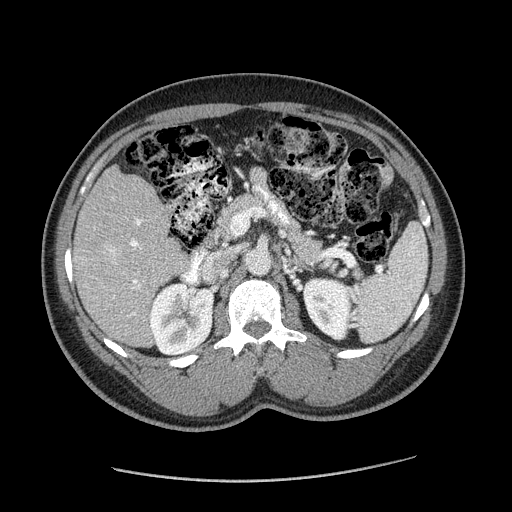
Contrast-enhanced abdominal CT (liver protocol), one axial slice. Position 85 of 182 along the scan axis. 120 kVp. Soft-tissue window (W 400 / L 40 HU). 512 × 512 image matrix, field of view 400 × 400 mm. From the clinical record (not read from this slice): diagnosis: hepatocellular carcinoma (patient treated with transarterial chemoembolisation; whether this scan precedes or follows treatment is not stated here); TNM stage (as recorded): Stage-I; Child-Pugh class: A.
Annotated regions visible in this slice (semi-automatically segmented with operator editing):
- liver parenchyma outside the tumour (the mass and vessels are separate outlines, so this box may not span the whole liver): bounding box (x1, y1, x2, y2) in pixels: (72, 166, 188, 346)
- mass: (98, 238, 127, 263)
- liver vessels: (114, 218, 142, 315)